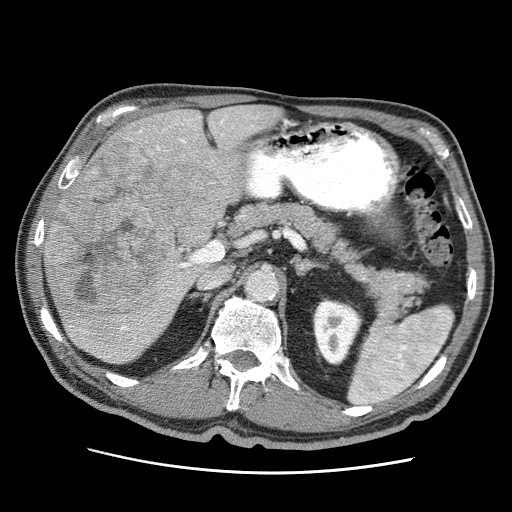
Contrast-enhanced abdominal CT (liver protocol), one axial slice; slice 25 of 75 in the series (ordered by position); 120 kVp; soft-tissue window (W 400 / L 40 HU); 2.5 mm slice thickness; 512 × 512 image matrix, field of view 360 × 360 mm. Case-level facts recorded for this patient, not image findings: diagnosis: hepatocellular carcinoma (patient treated with transarterial chemoembolisation; whether this scan precedes or follows treatment is not stated here); TNM stage (as recorded): Stage-IIIA; Child-Pugh class: A; tumour nodularity: multinodular; tumour size: 13.9 cm.
Outlined on this slice (semi-automatically segmented with operator editing):
- liver parenchyma outside the tumour (the mass and vessels are separate outlines, so this box may not span the whole liver): bounding box (x1, y1, x2, y2) in pixels: (44, 106, 281, 362)
- mass: (47, 137, 229, 345)
- liver vessels: (120, 115, 253, 342)